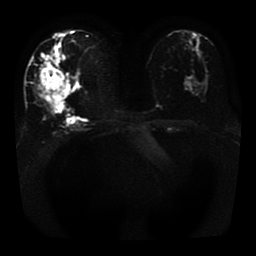
Breast MRI, one axial slice; slice 19 of 41 in the series (ordered by position); diffusion-weighted series; image 2 of 4 stored at this slice position (different b-values; order by instance number); 1.5 T; 256 × 256 image matrix. Female patient.
Annotated regions visible in this slice (outlined manually by an expert reader):
- tumour on diffusion-weighted imaging: box from (x=38, y=53) to (x=70, y=104) px